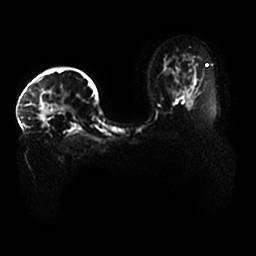
Breast MRI, one axial slice. Slice 25 of 33 in the series (ordered by position). Diffusion-weighted series; image 2 of 4 stored at this slice position (different b-values; order by instance number). 1.5 T. 4 mm slice thickness. 256 × 256 image matrix, field of view 400 × 400 mm. Female patient.
Structures marked on this image (expert manual segmentation):
- tumour on diffusion-weighted imaging: box from (x=38, y=101) to (x=76, y=124) px